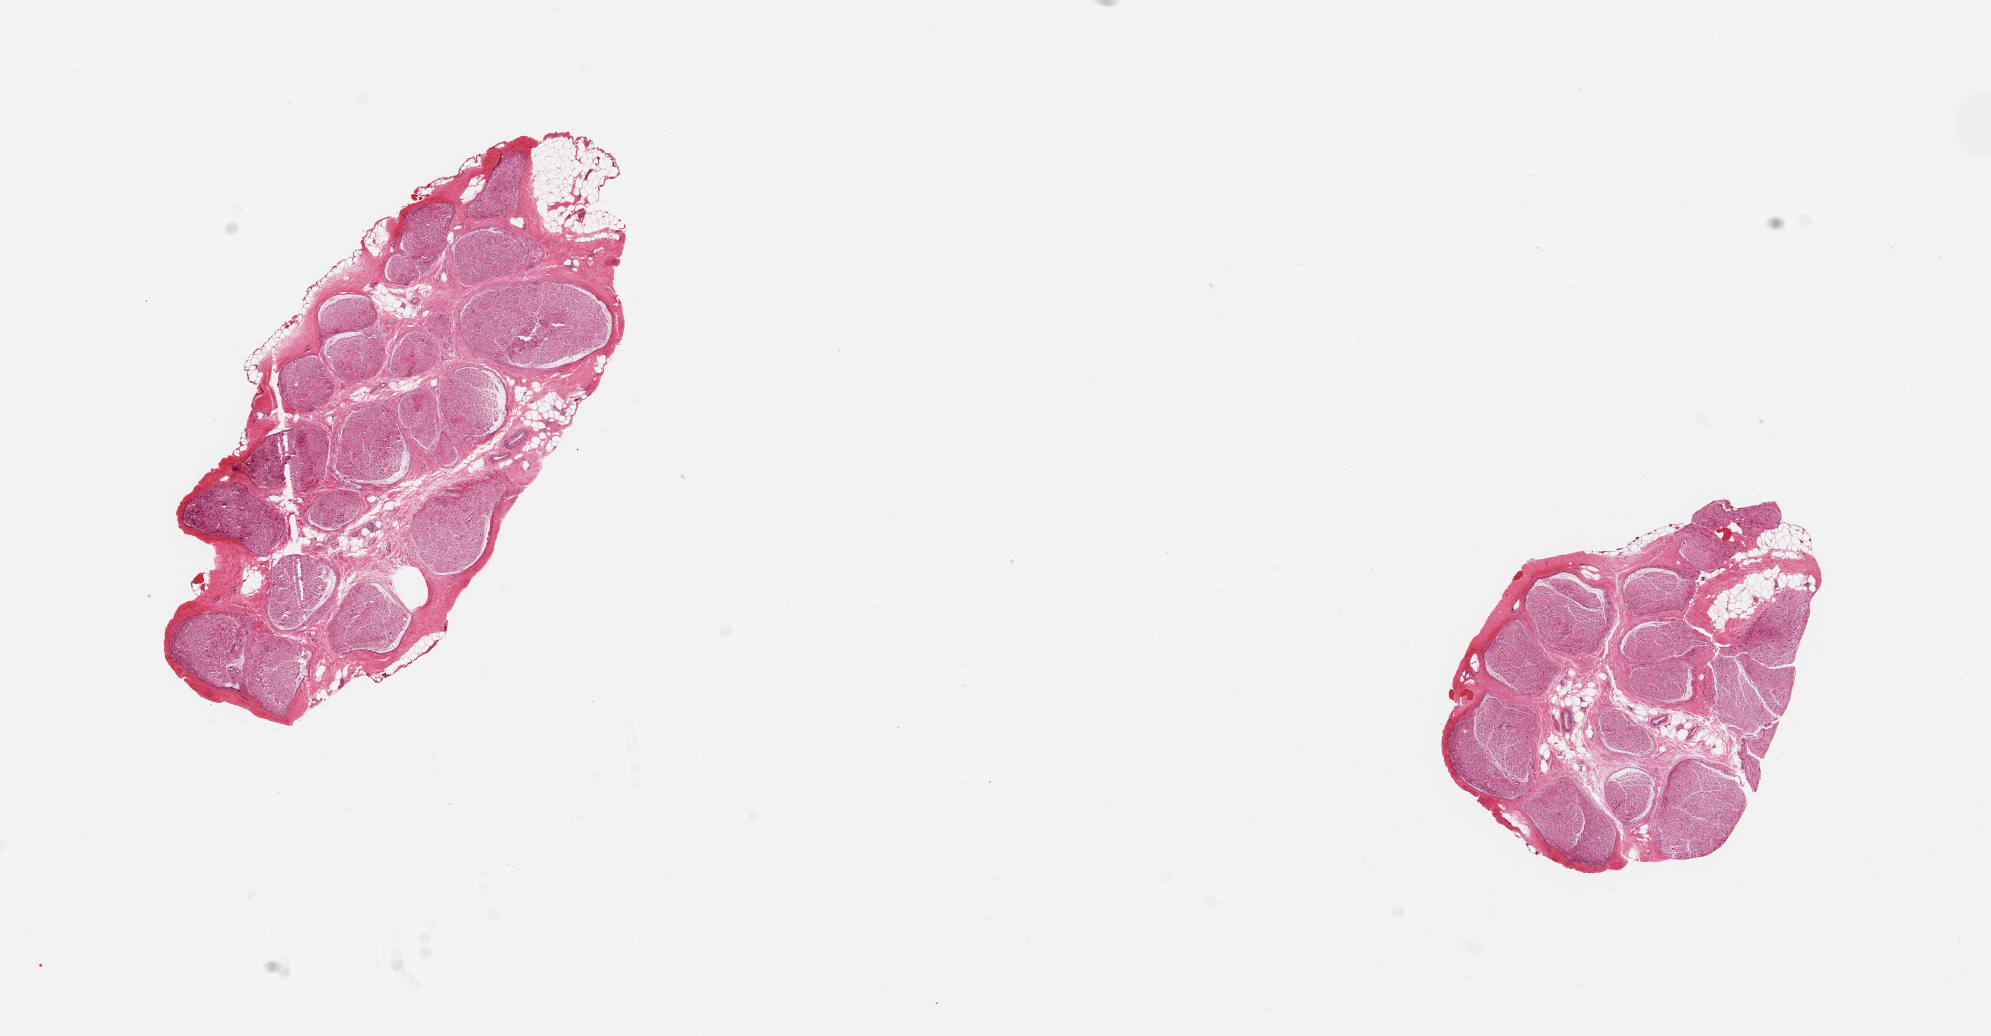
Whole-slide image, hematoxylin and eosin (H&E) stain — low-resolution overview of the scanned area, about 15.8 x 8.2 mm (acquisition: 20x scan), PAXgene-fixed, paraffin-embedded tissue, target tissue: tibial nerve, tissue donor sample.
• pathologist's review note for this sample: 2 pieces; 10% fat content